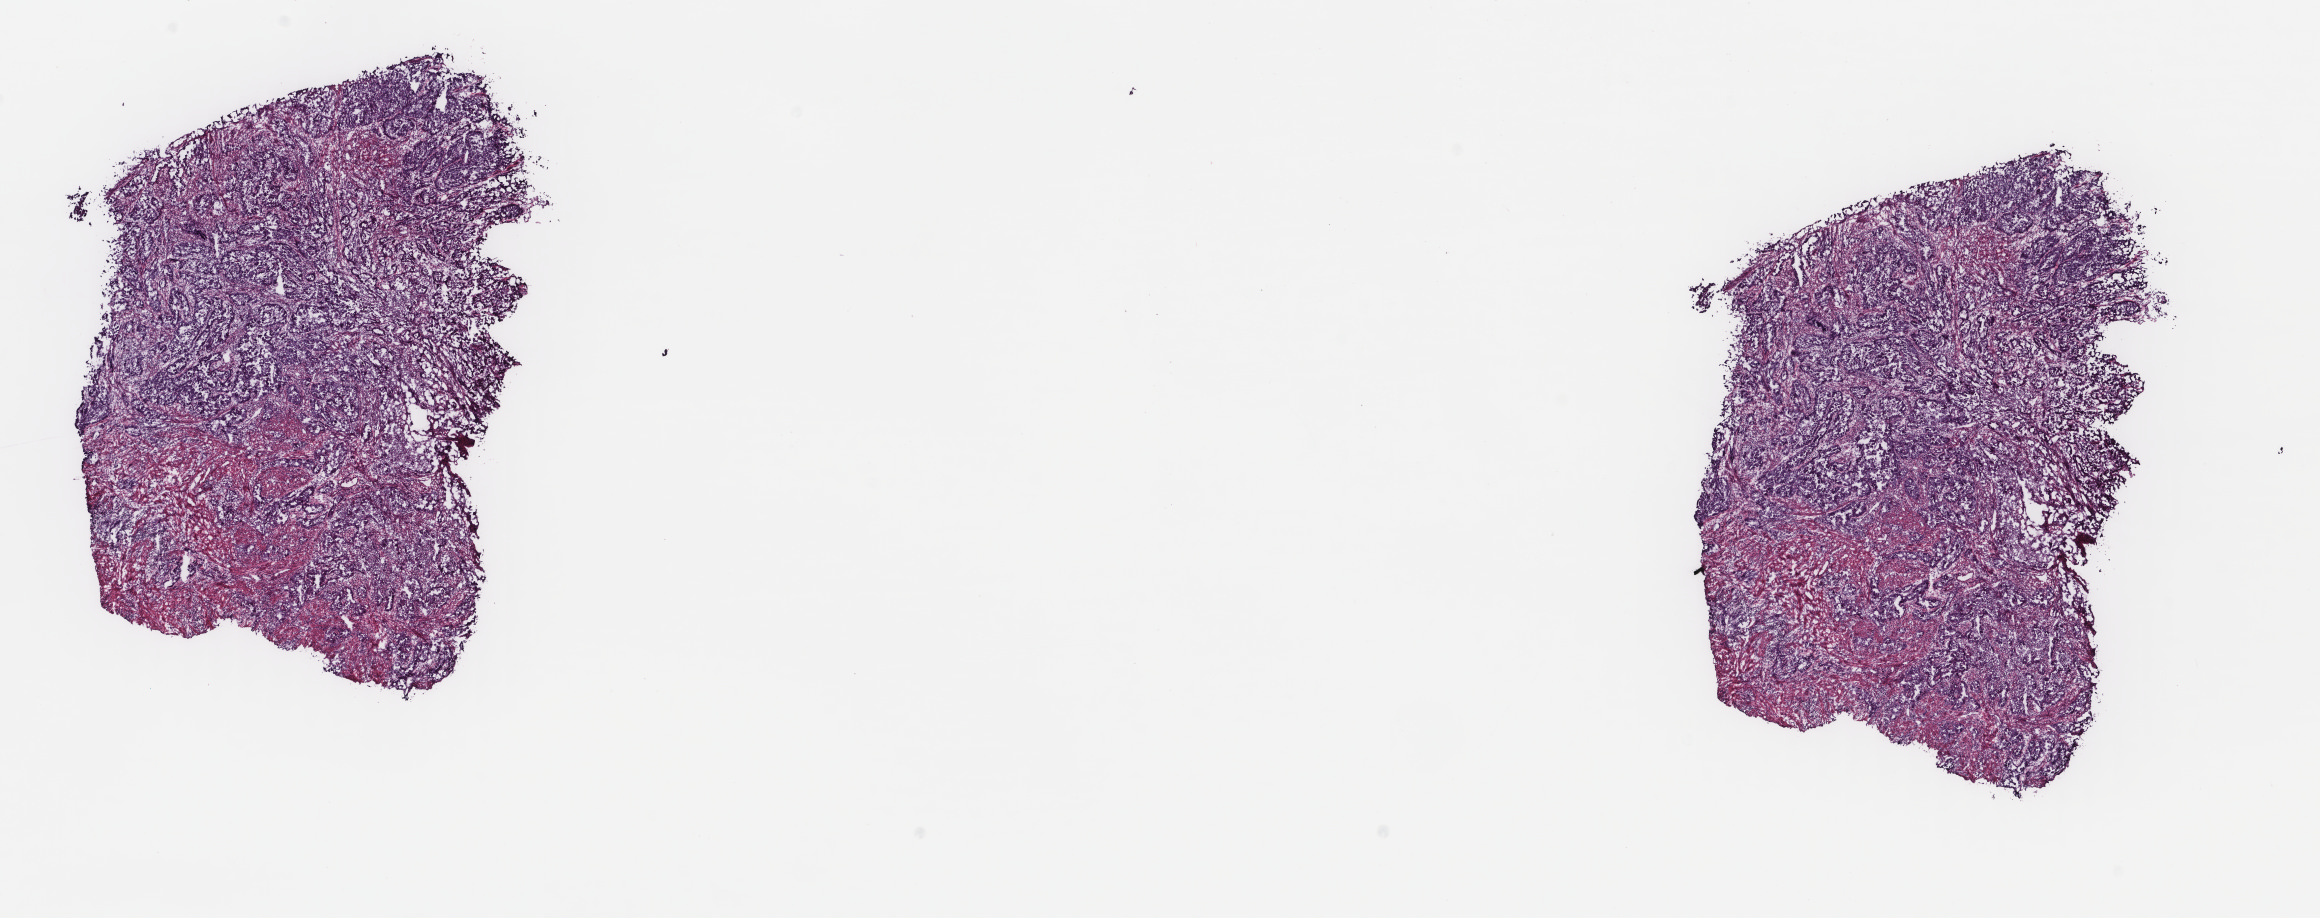
Digitized Hematoxylin and eosin (H&E) stained tissue section (whole slide), a low-resolution overview of the entire scanned area, about 18.4 x 7.3 mm (slide scanned at 40x), frozen section from the top of the tissue portion, primary tumour sample from the uterus. Patient: female, age at initial diagnosis 72 years. Histologic grade: G3 (poorly differentiated). Composition of this section per pathologist review: tumour cells 60%, tumour nuclei 60%, normal cells 0%, stromal cells 30%, necrosis 10%. Infiltration values recorded for this section: lymphocyte infiltration 60%, monocyte infiltration 20%, neutrophil infiltration 10%.
• histologic diagnosis: Serous cystadenocarcinoma, NOS (endometrium)
• FIGO stage: IB